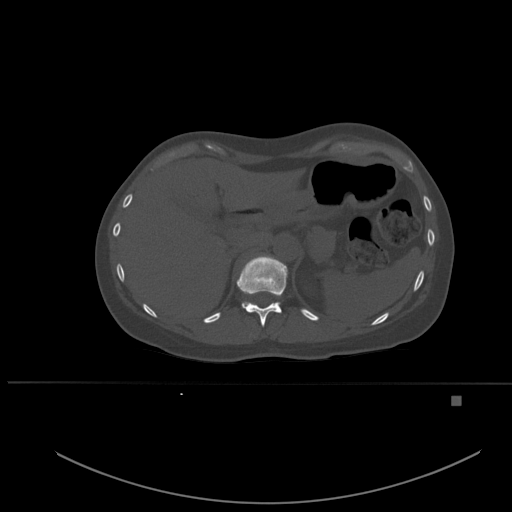
CT including the spine, one axial slice. Position 269 of 651 along the scan axis. Bone window (W 1800 / L 400 HU). 1.5 mm slice thickness. 512 × 512 image matrix. Patient: female, 49 years. From the clinical record (not read from this slice): primary cancer: breast; vertebrae with lytic lesions (as recorded): L3, T12, L4.
Structures marked on this image (semi-automatically segmented with operator editing):
- T11 vertebra: bounding box (x1, y1, x2, y2) in pixels: (236, 255, 288, 327)
- T12 vertebra: (242, 302, 253, 308)